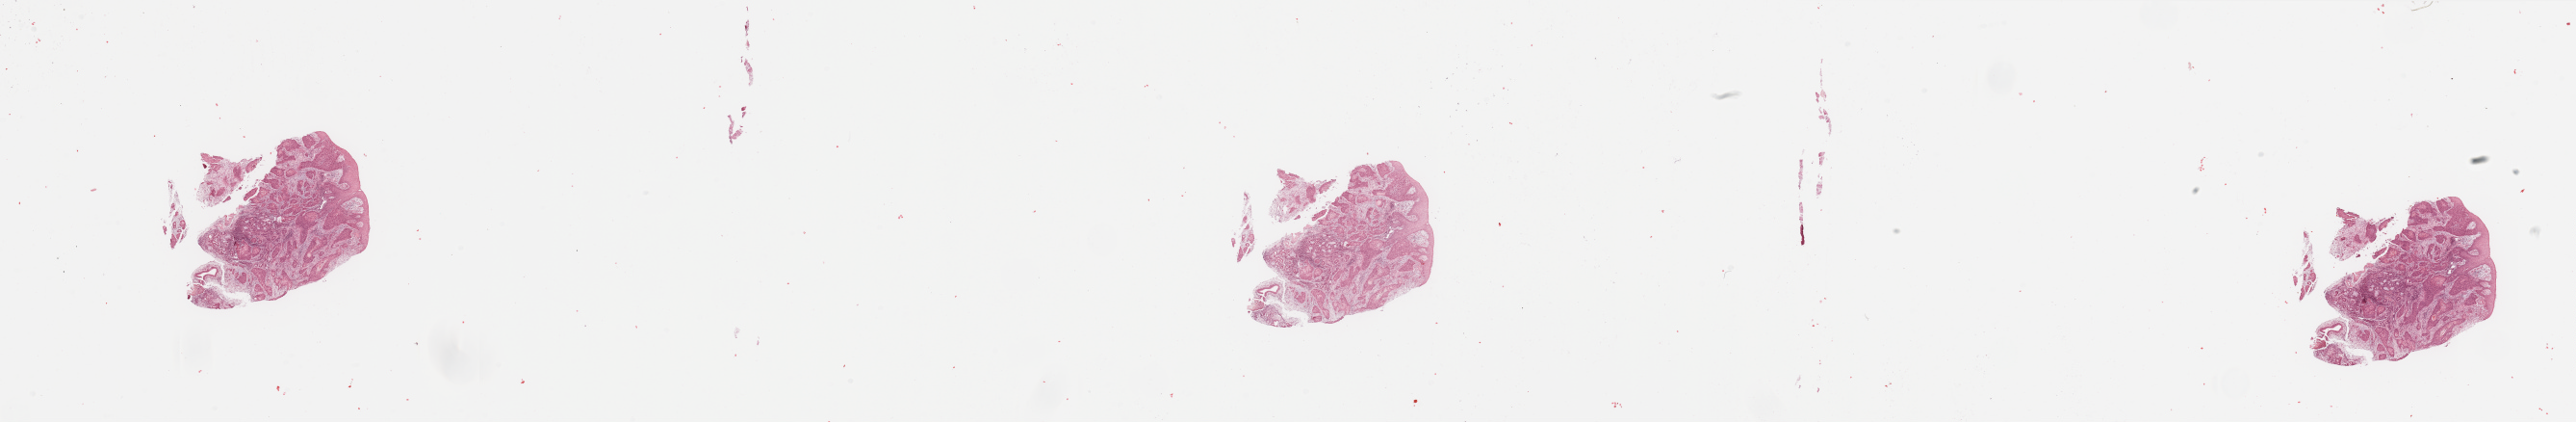
Hematoxylin and eosin (H&E) stained whole-slide image, shown as a low-resolution overview of the whole scanned area (about 42.3 x 6.9 mm, acquisition: 20x scan). Tumour tissue sample, sampled site: floor of mouth. Male, 58 y/o. Histologic grade: G2 (moderately differentiated). Pathologist review of this section (percent, as recorded): tumour nuclei 80%, necrosis 0%.
AJCC pathologic stage: I. Diagnosis: Squamous cell carcinoma, NOS (floor of mouth, NOS).